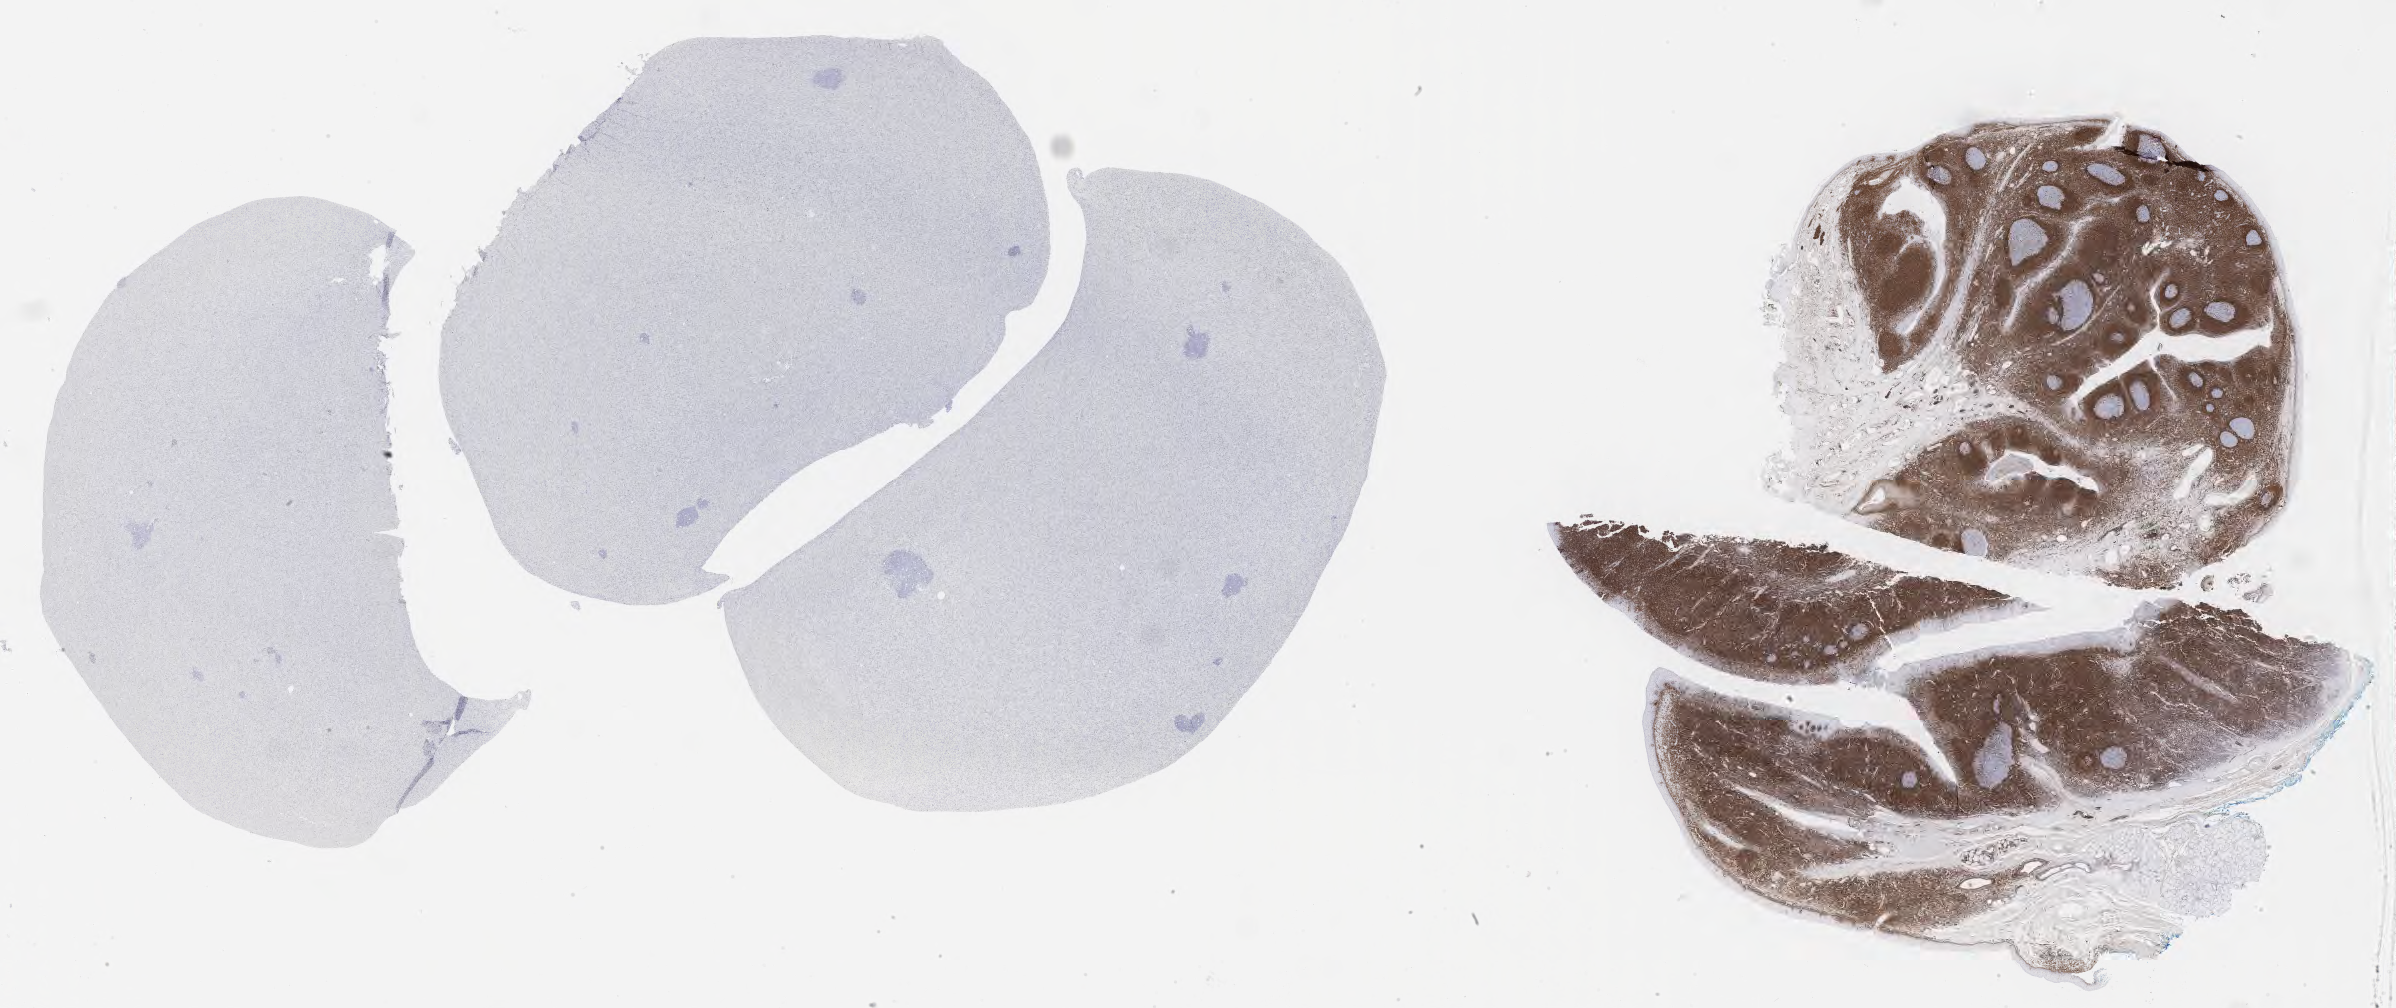
IHC for BCL2, whole-slide image, whole scanned area (about 38.7 x 16.3 mm) shown as a low-resolution overview. Tumor tissue. Male patient, aged 17.
Histologic diagnosis: Burkitt lymphoma, NOS.